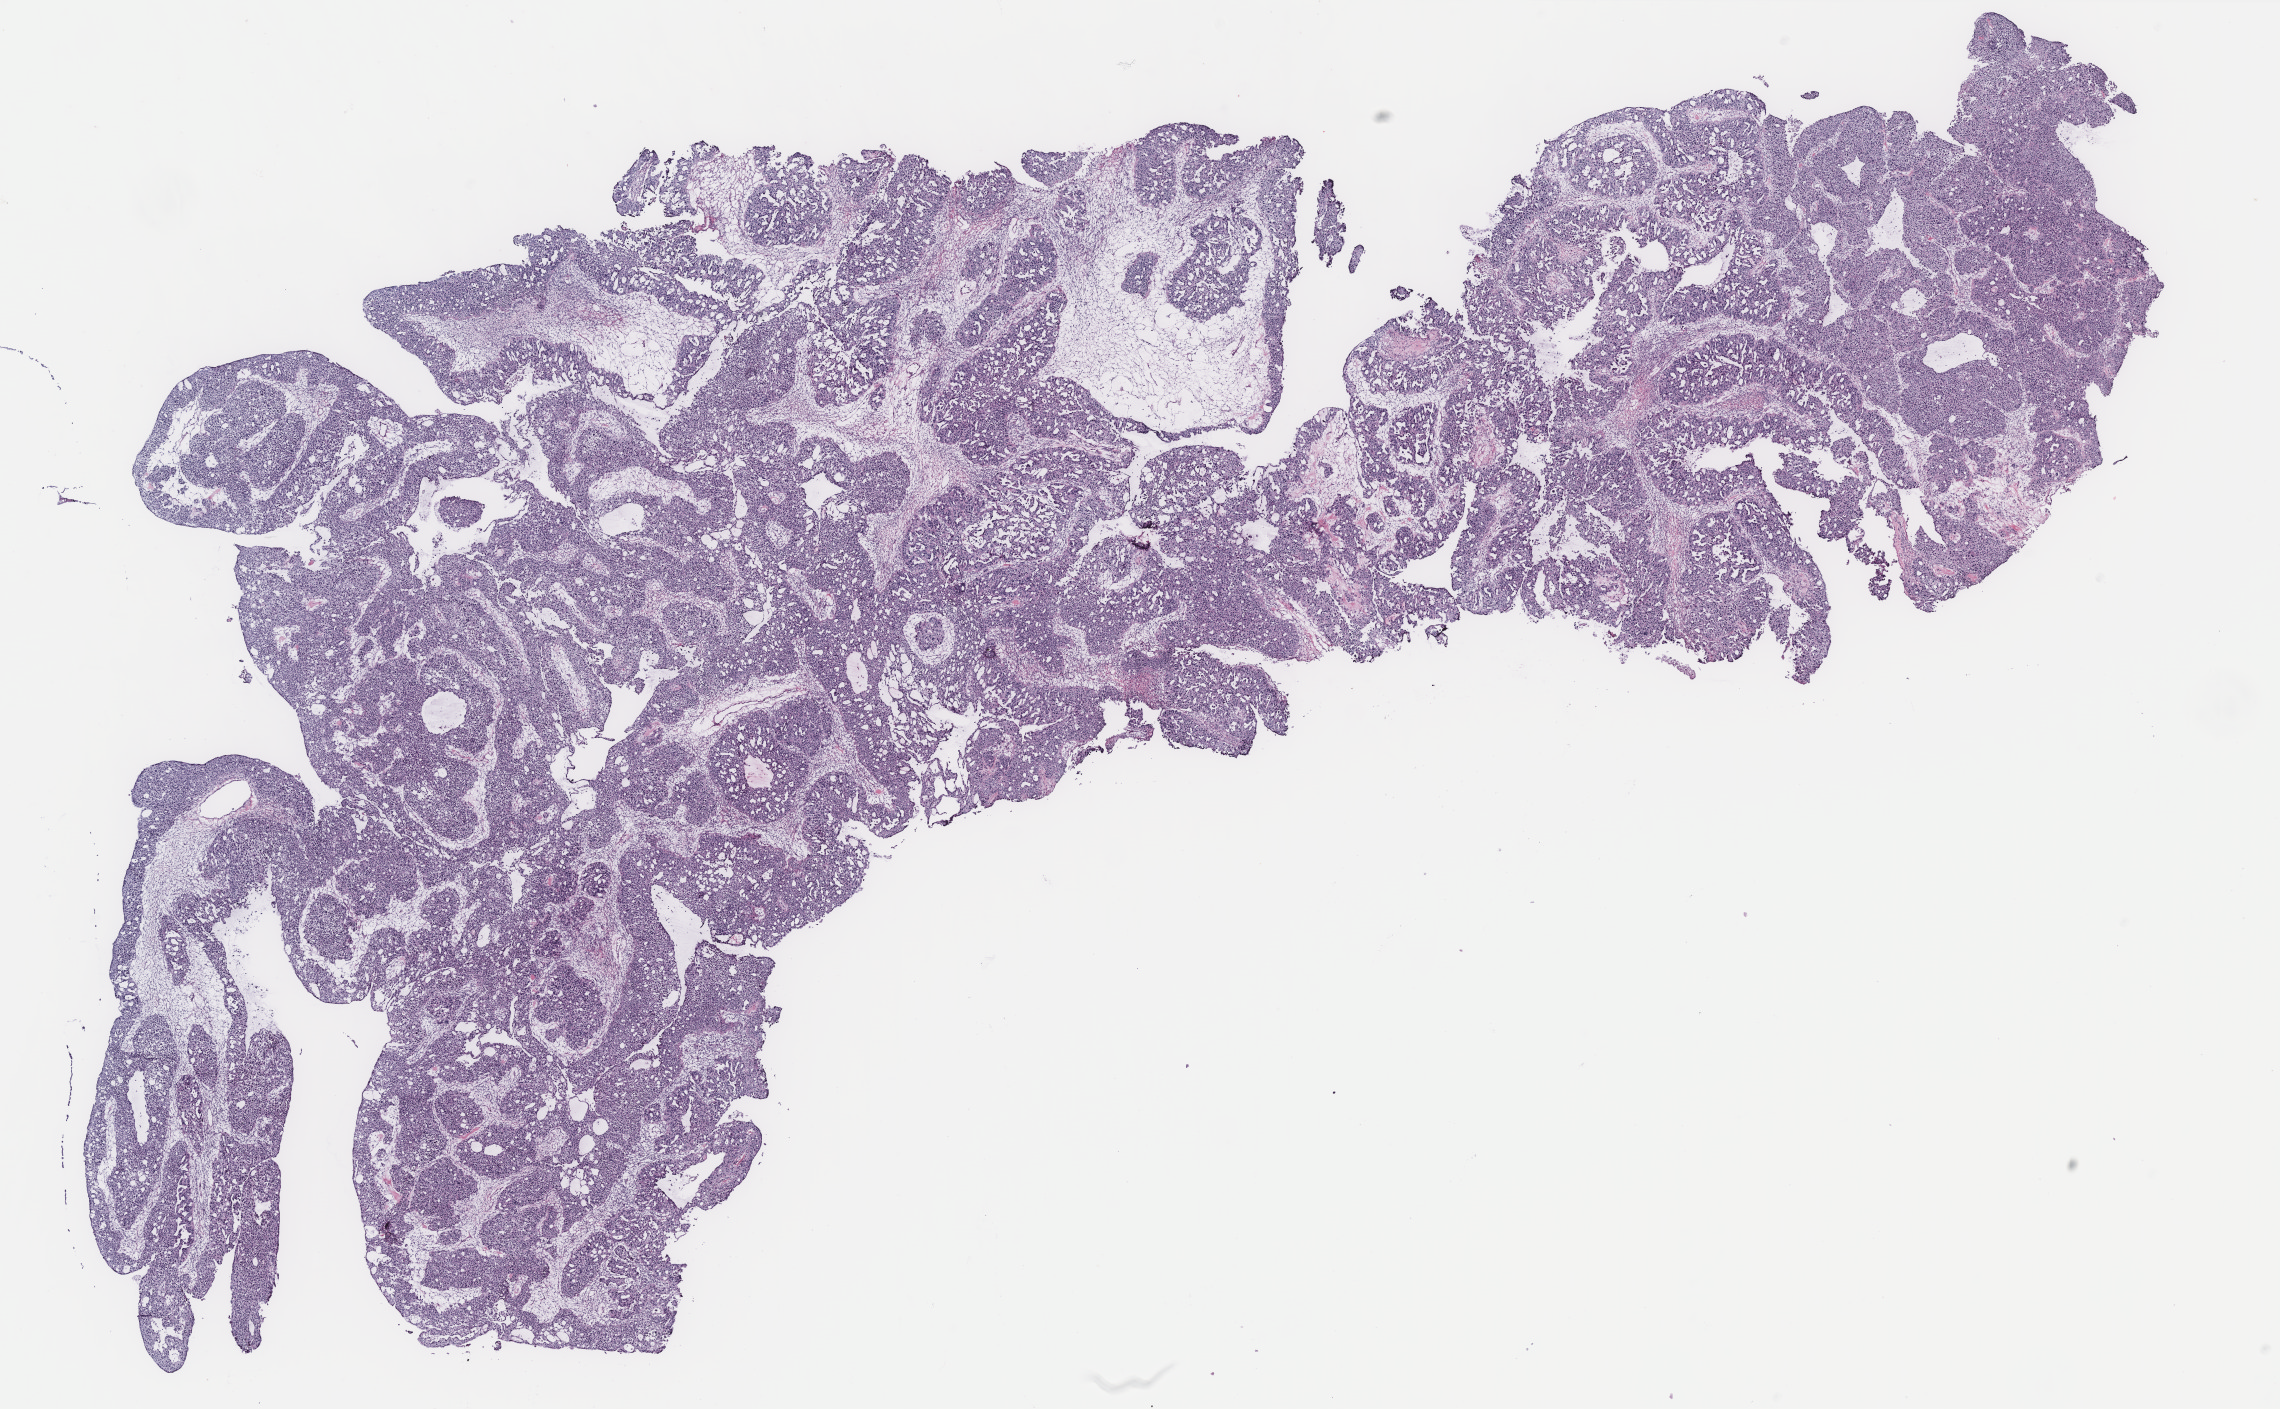
Digitized H&E-stained tissue section (whole slide) — low-resolution overview of the scanned area, about 18.2 x 11.3 mm; tumour tissue sample, ovary. Patient: female, age 70 years.
Histologic diagnosis: Serous adenocarcinoma, NOS.